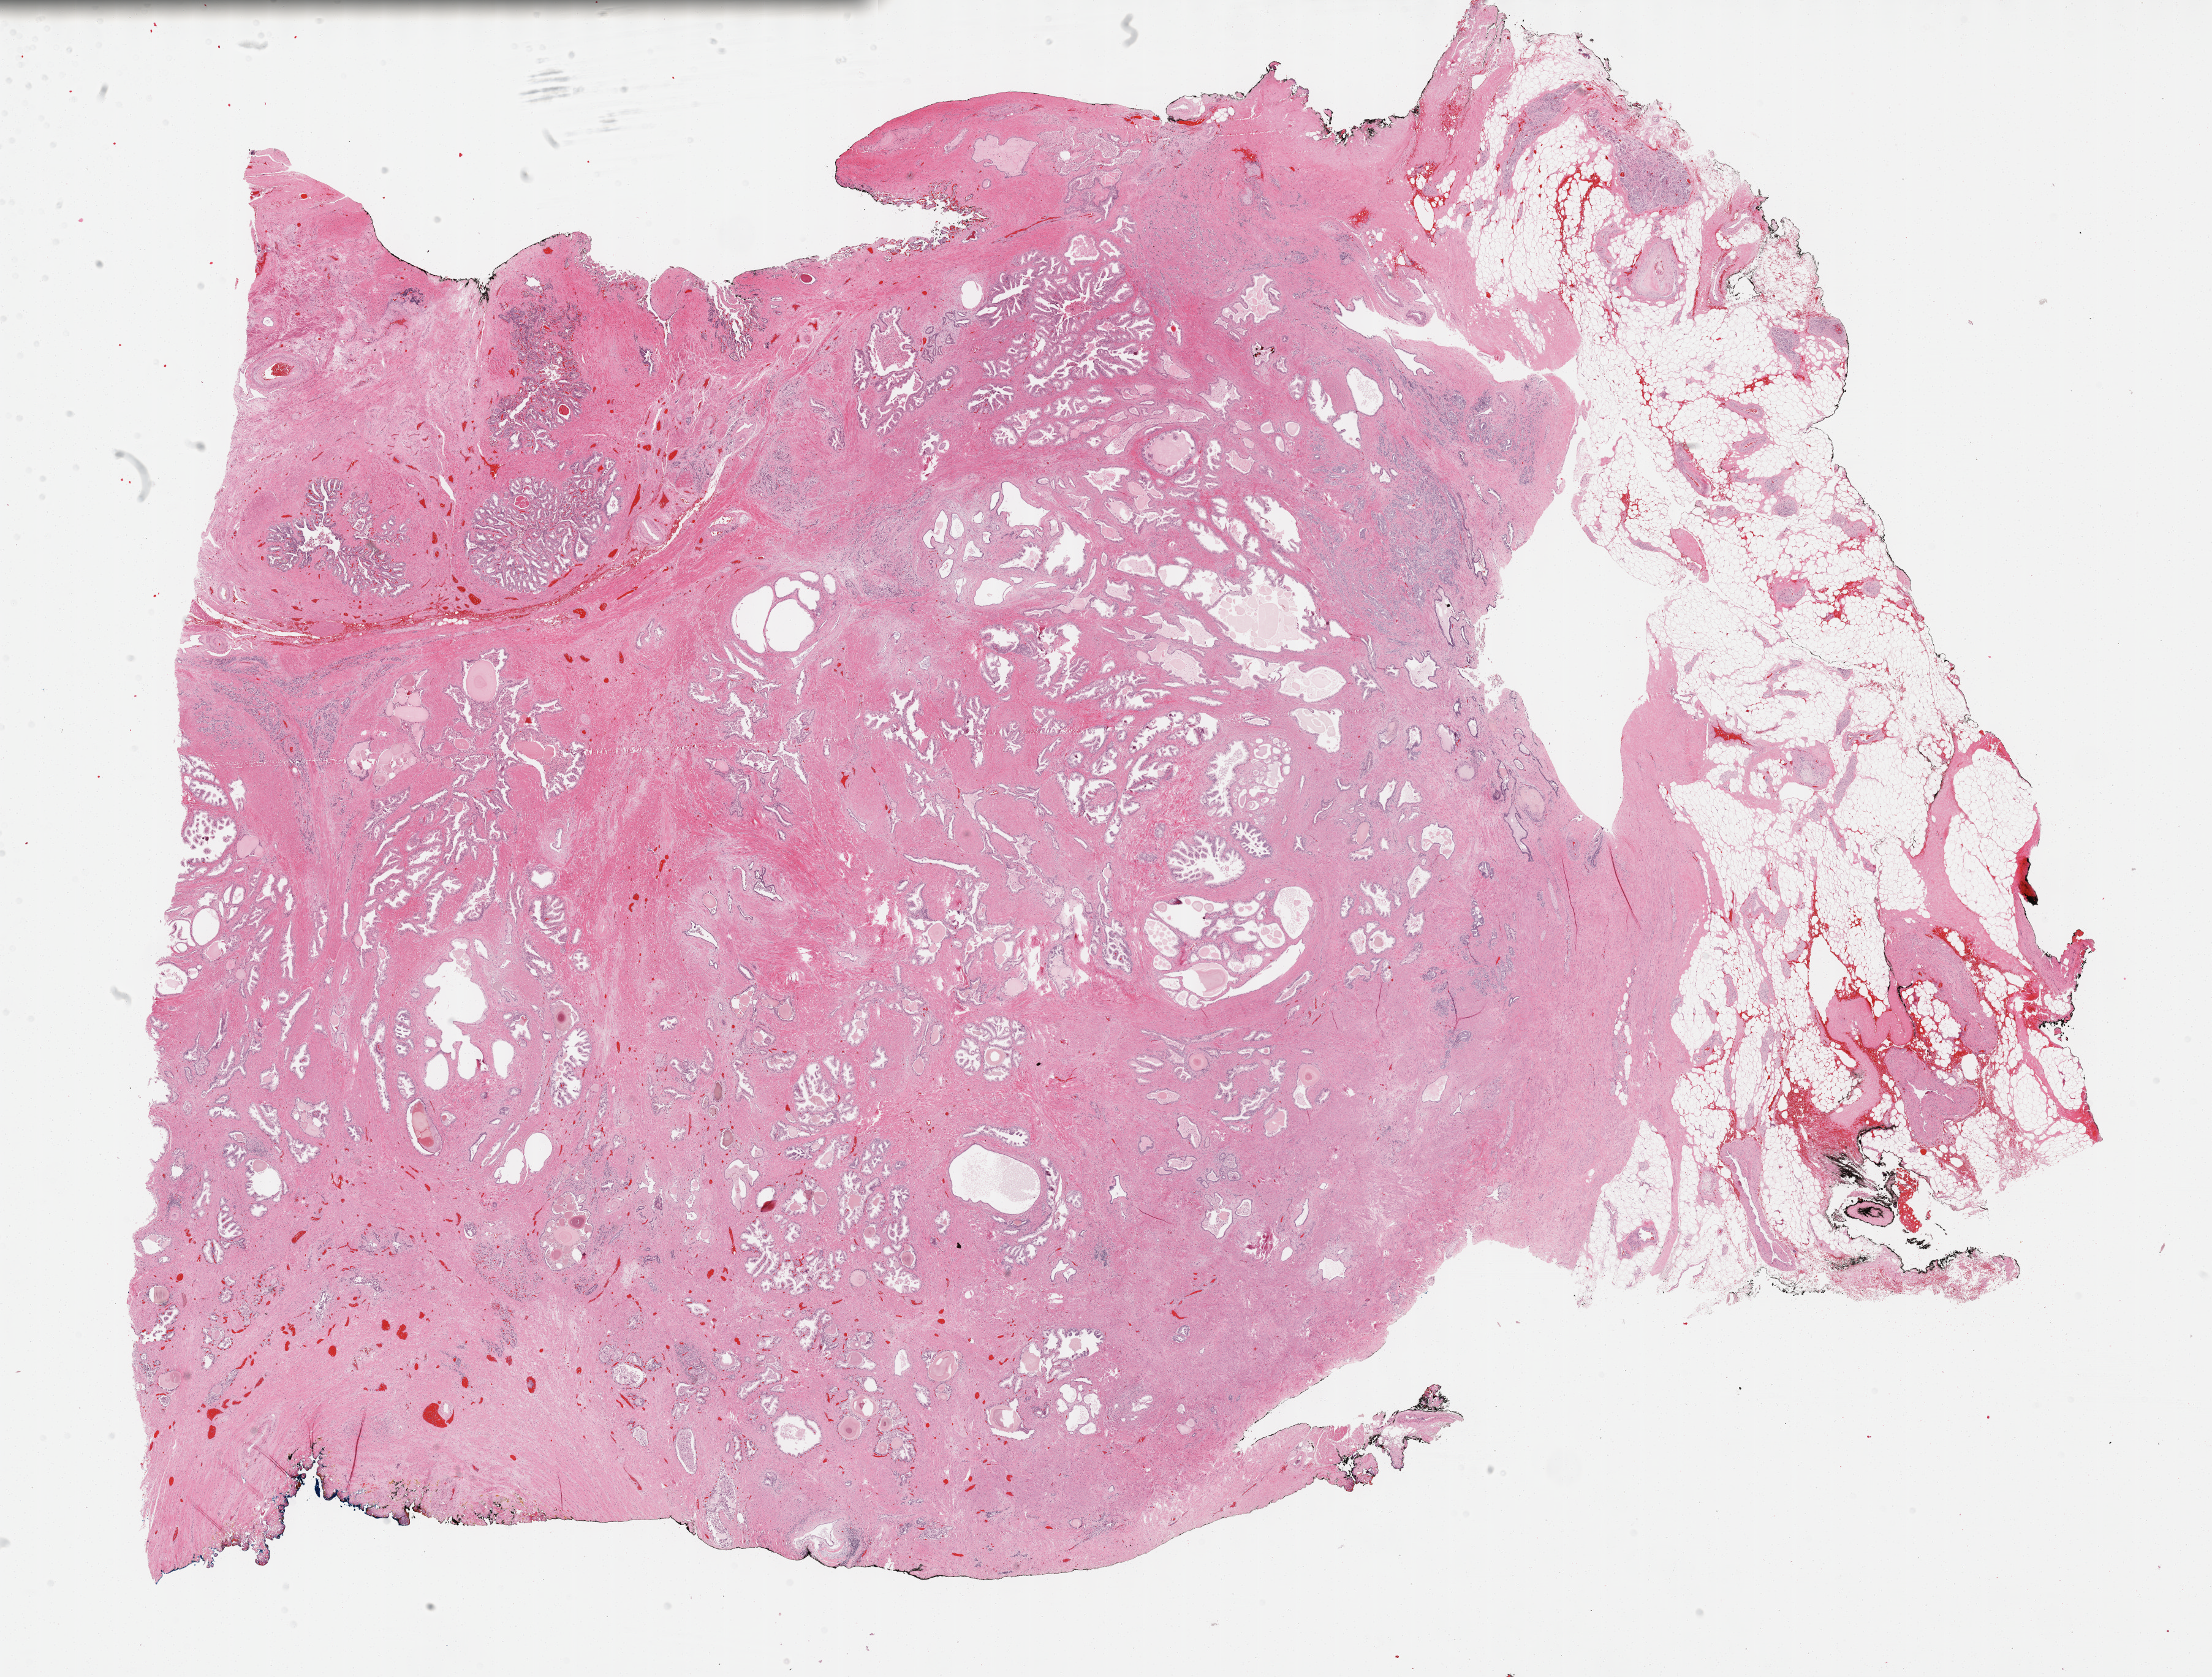
Whole-slide histology image, H&E-stained, shown as a low-resolution overview of the whole scanned area (about 29.2 x 22.1 mm, from a 40x scan), FFPE section, prostate, primary tumour sample. Patient: male, age at initial diagnosis 65 years. Gleason score: 9 (4+5).
• pathologic diagnosis: Adenocarcinoma, NOS (prostate gland)
• lymph nodes positive (case pathology): 0 of 3 examined